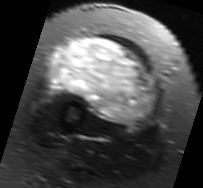
MRI of an extremity soft-tissue mass, one axial slice. Slice 32 of 91 in the series (ordered by position). T2-weighted fat-saturated. MR volume resampled by the dataset authors to the PET/CT grid (not the native acquisition matrix). 3.27 mm slice thickness. 203 × 188 image matrix, field of view 198 × 184 mm. Female patient. Case-level facts recorded for this patient, not image findings: histological type: malignant solitary fibrous tumor; grade: intermediate; site of the primary tumour: right thigh.
Outlined on this slice (expert contour drawn on MRI and transferred to this co-registered scan by the dataset authors):
- gross tumour volume including surrounding oedema: box from (x=46, y=37) to (x=159, y=127) px
- gross tumour volume (mass): (x=51, y=37)–(x=155, y=123)